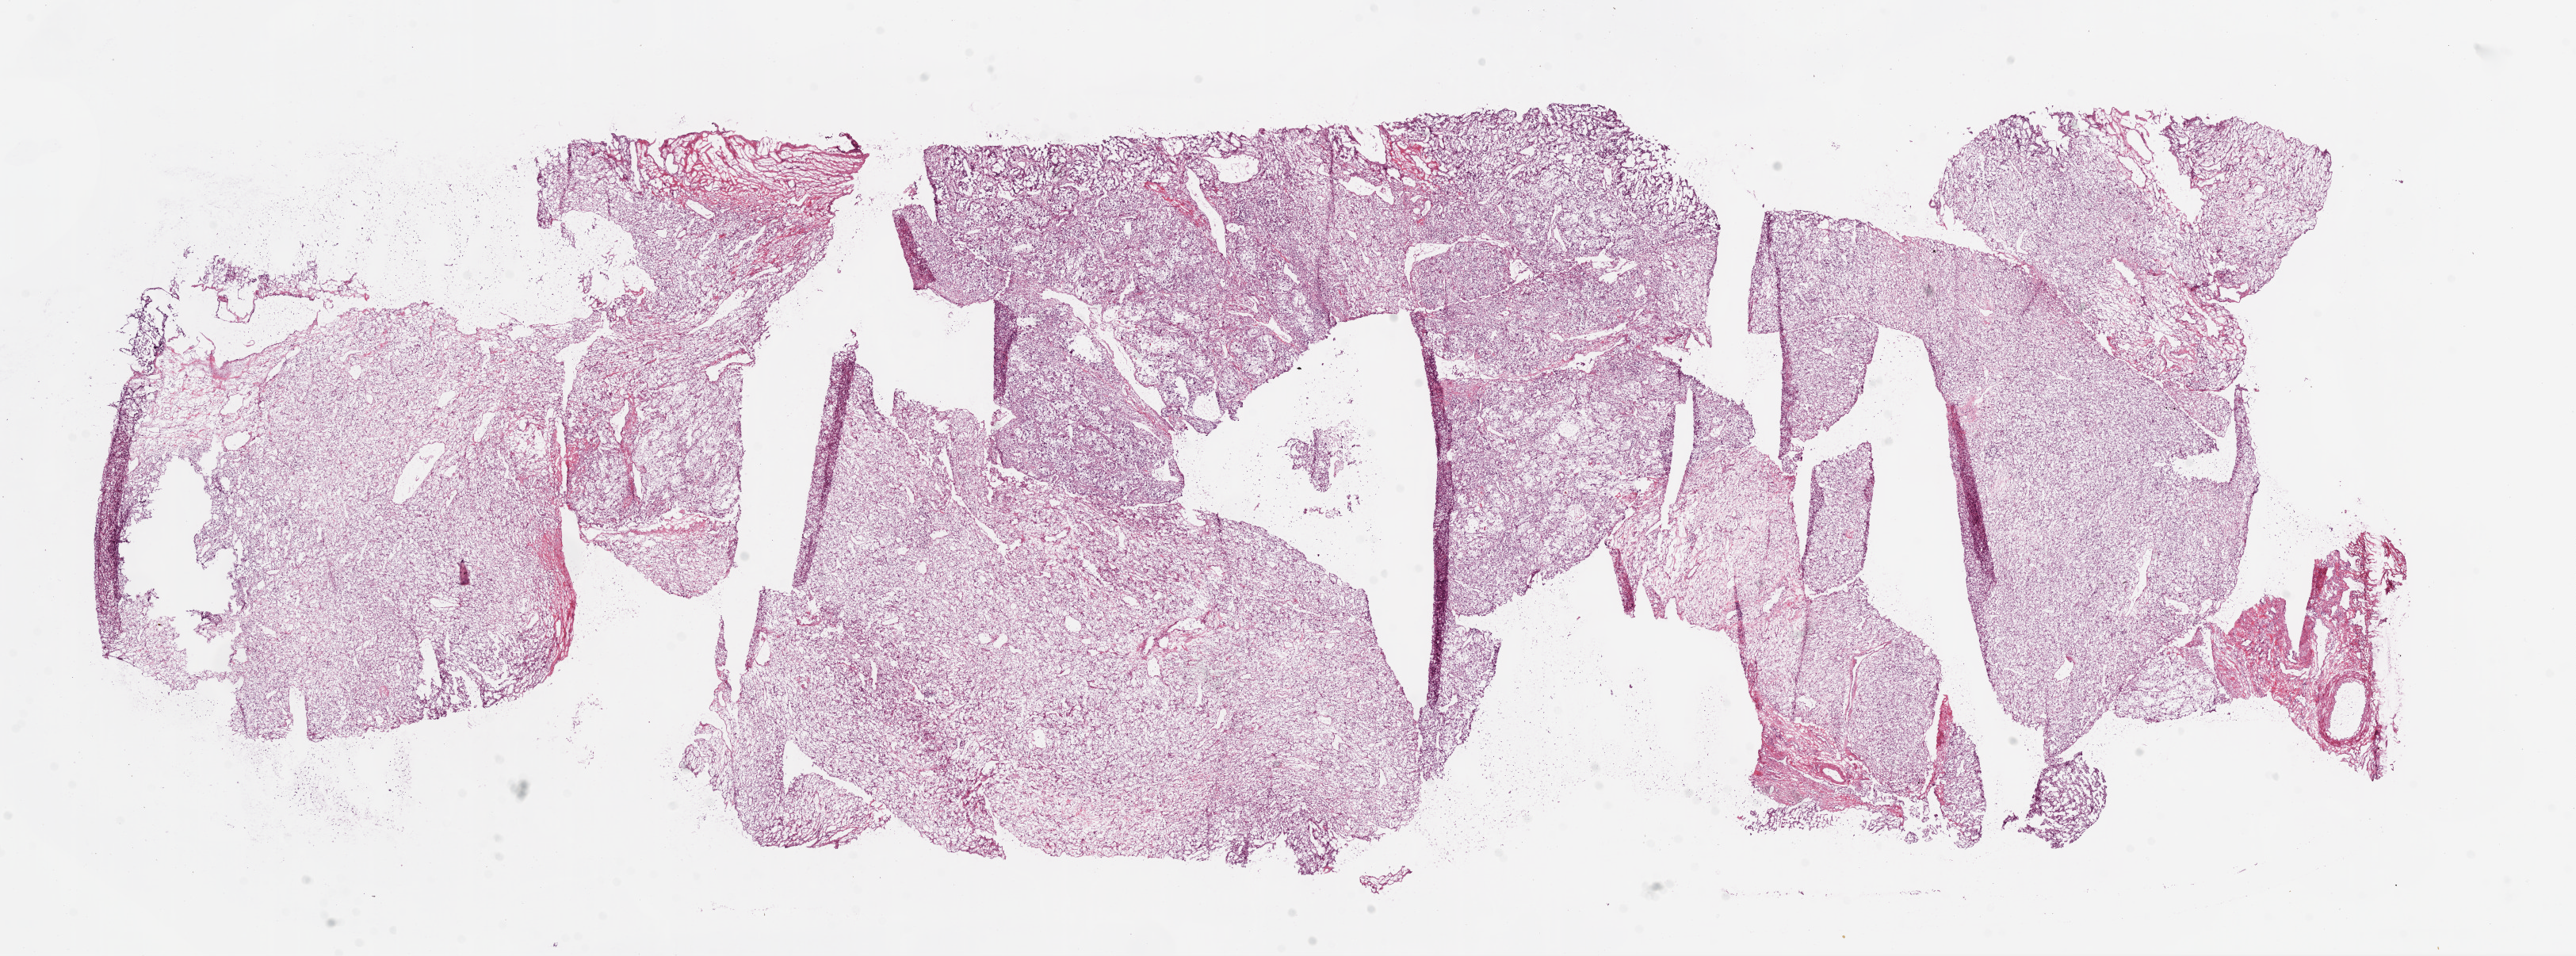
Whole-slide histology image, H&E-stained, a low-resolution overview of the entire scanned area, about 26.1 x 9.7 mm (slide scanned at 20x), frozen section, primary tumour sample from the kidney. Male patient; age at initial diagnosis 51 years.
Histologic diagnosis: Clear cell adenocarcinoma, NOS.